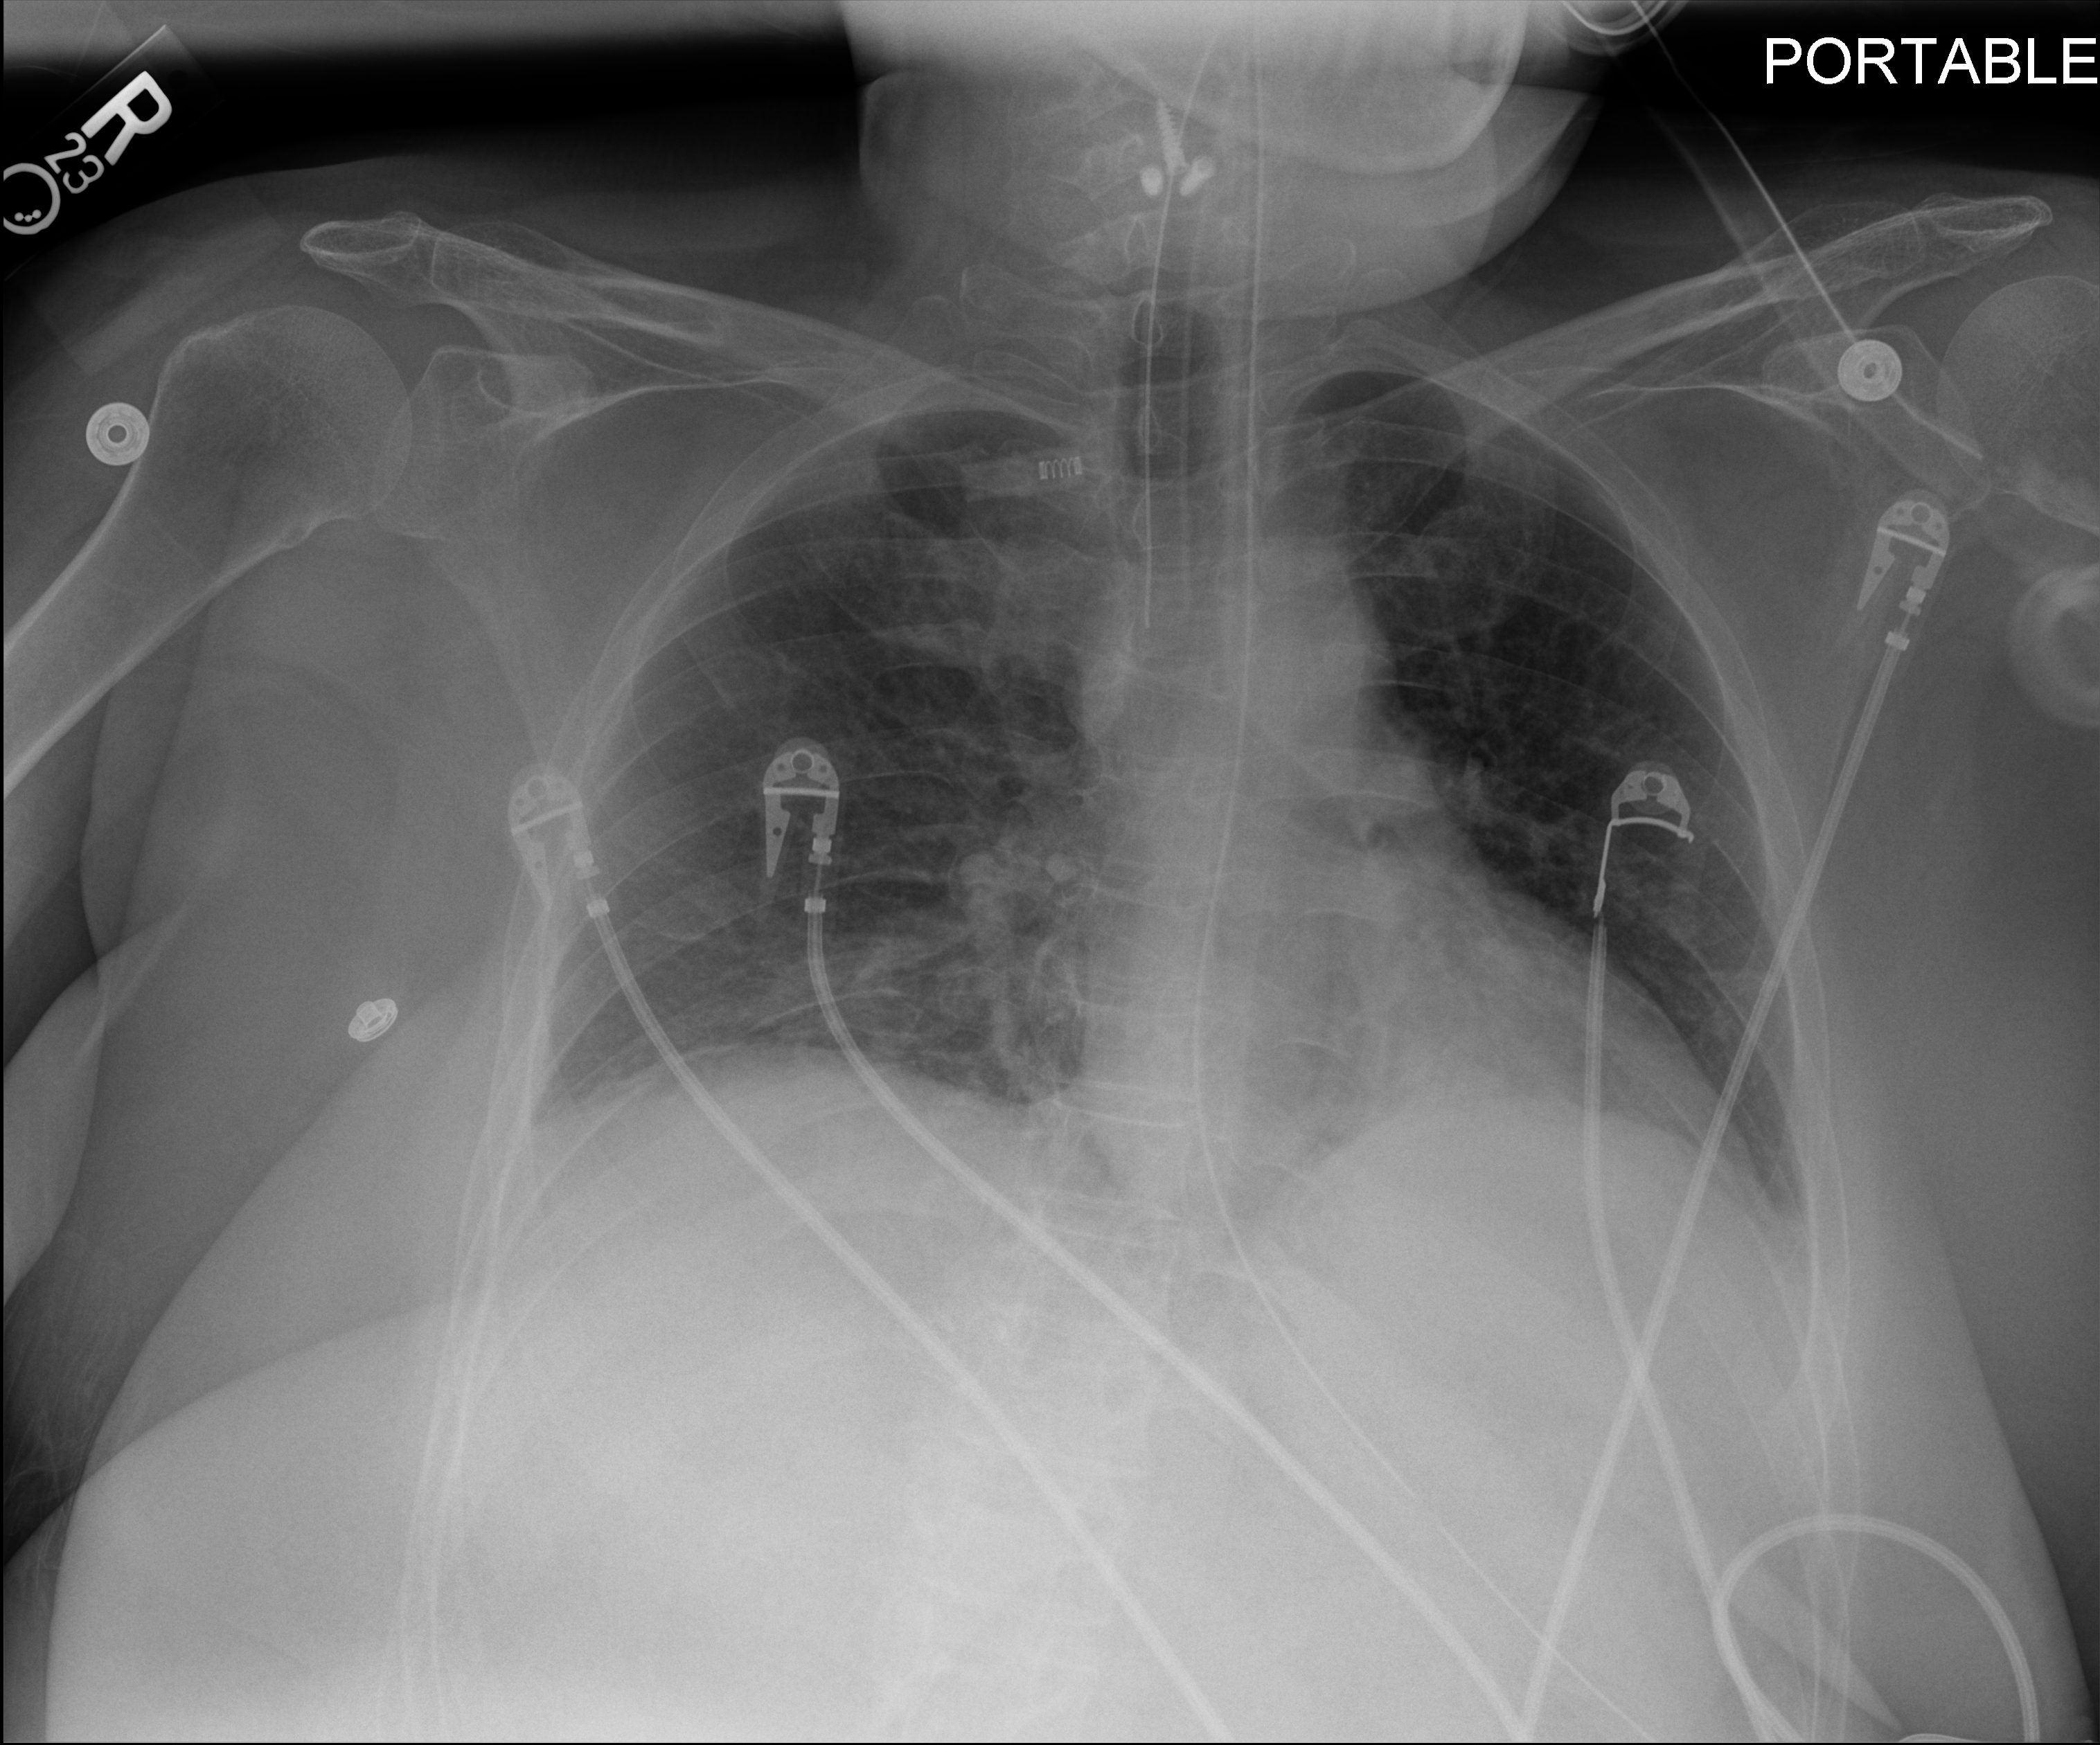
Chest X-ray (portable). Female patient hospitalised with COVID-19, age 18–59 years.
From the hospital-stay record, not from the radiograph (when in the stay this image was taken is not recorded):
- mechanically ventilated during this hospital stay: no